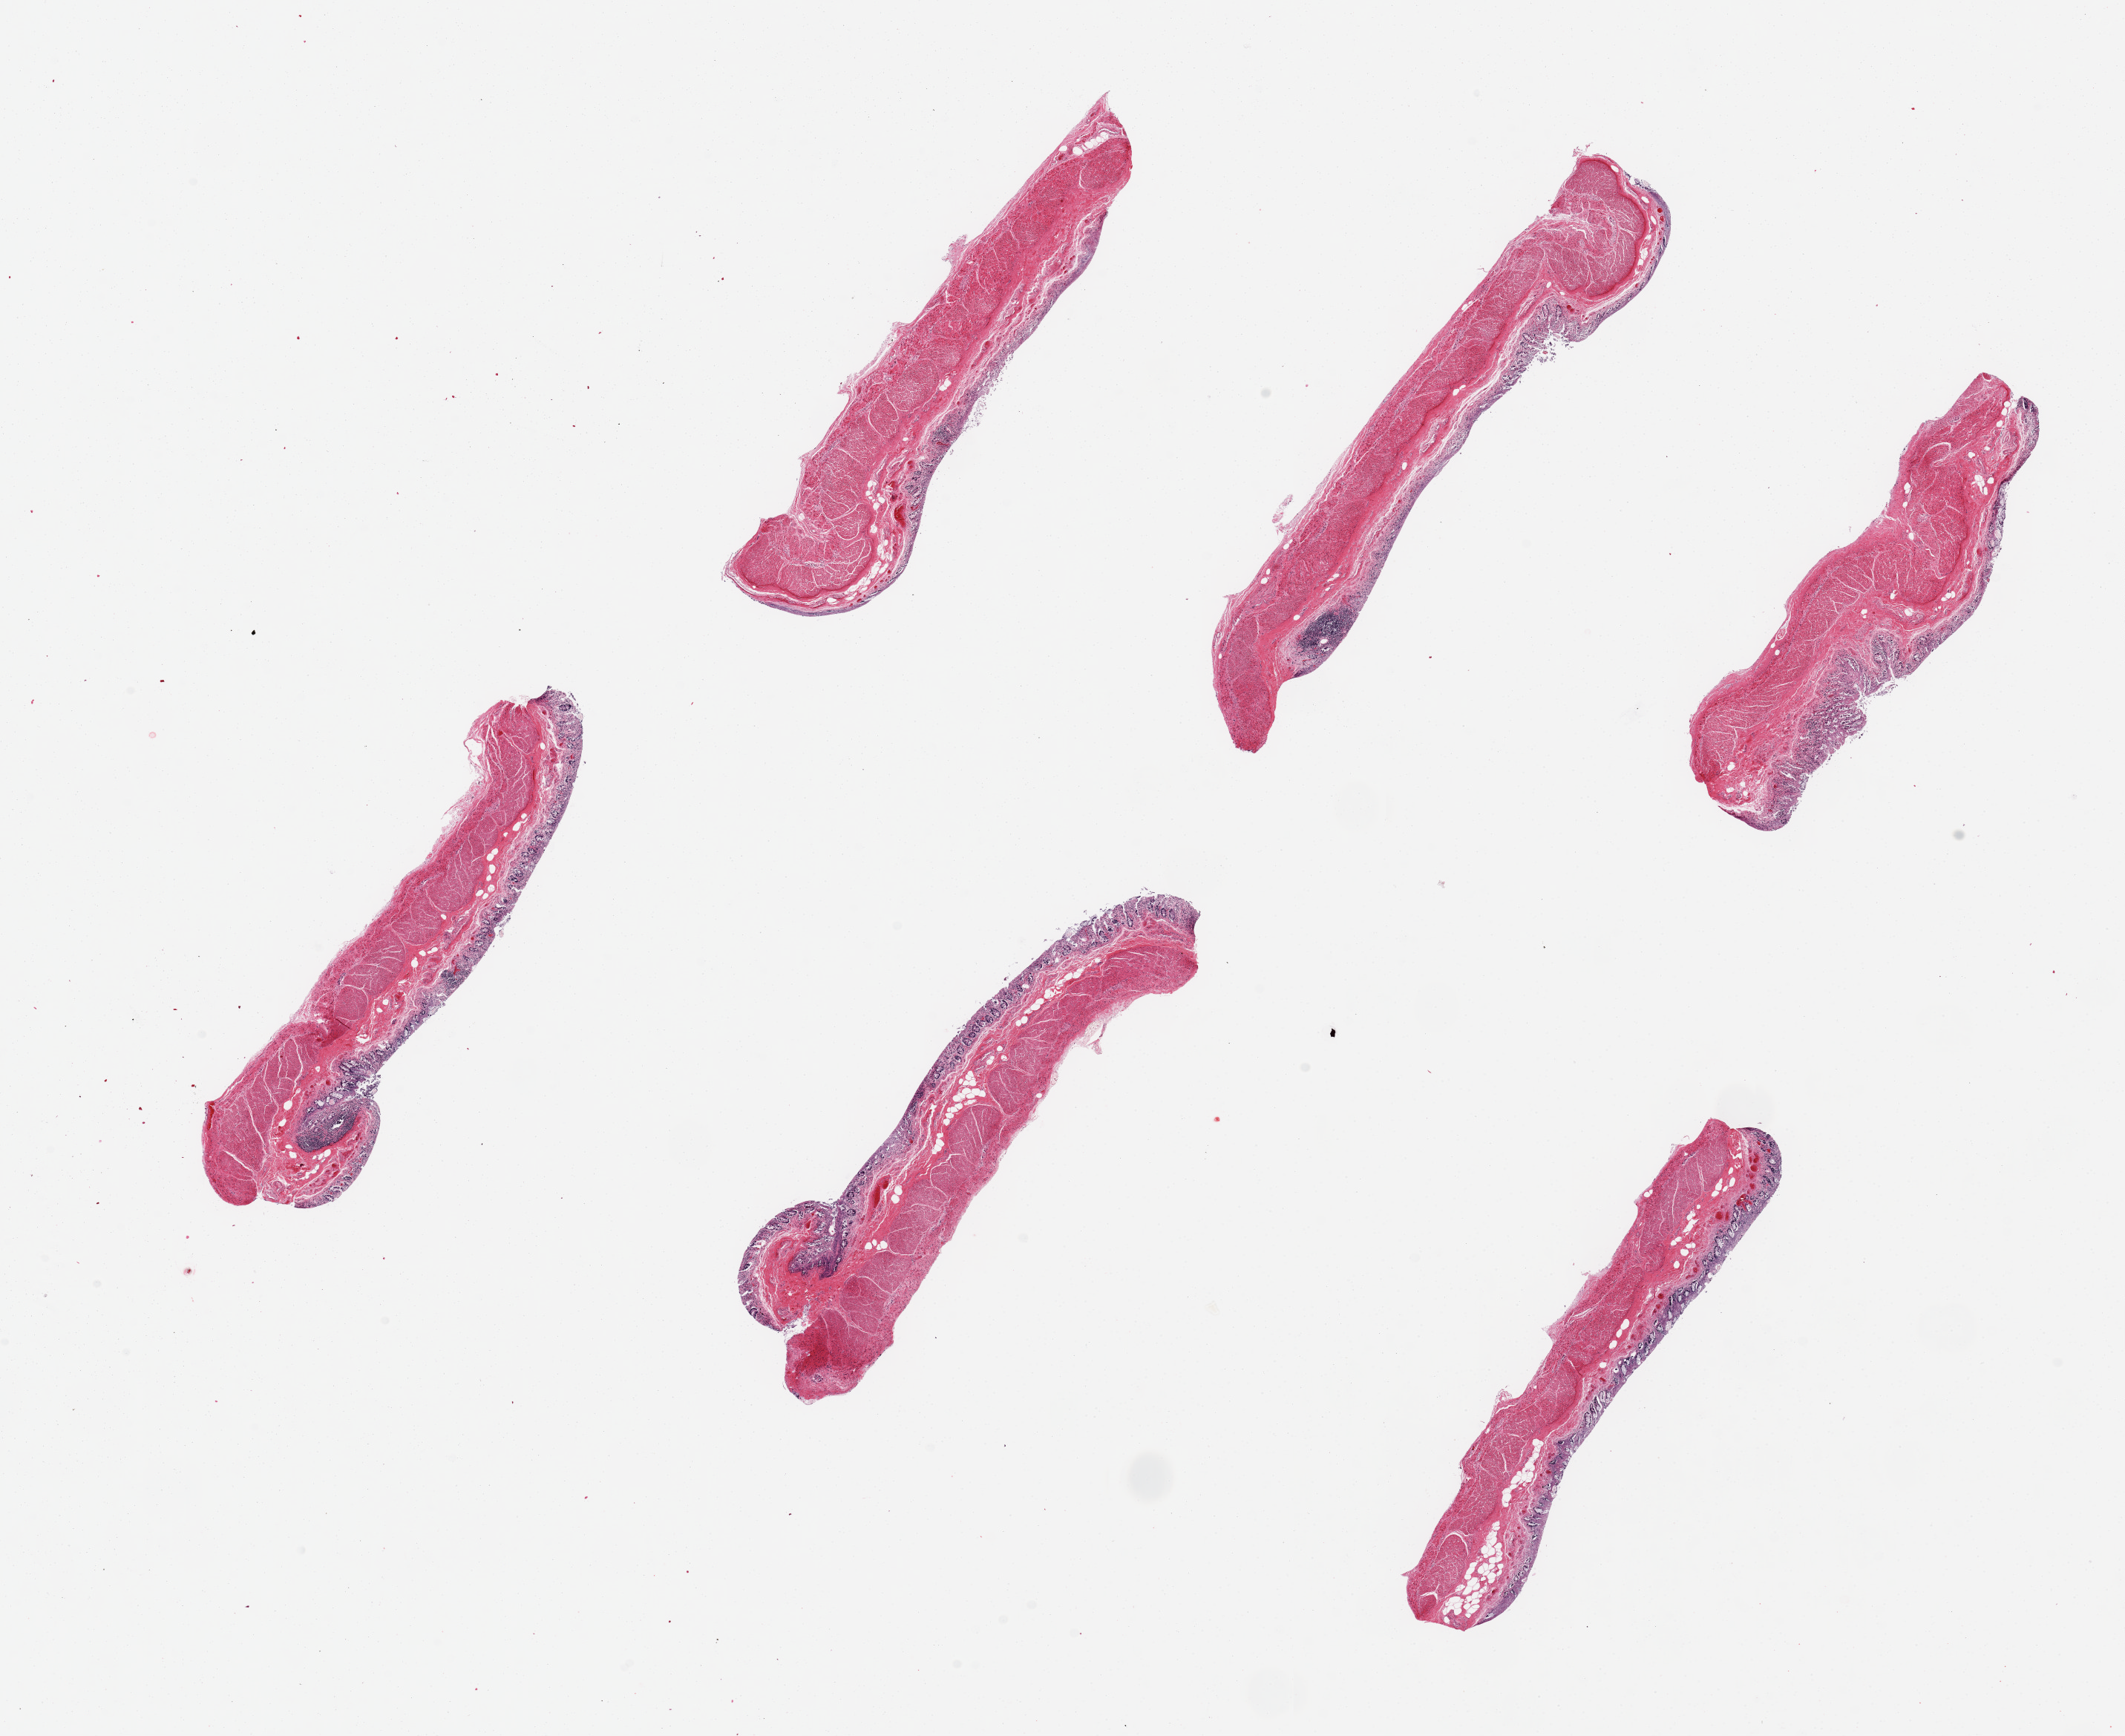
Digitized hematoxylin and eosin (H&E)-stained section, brightfield, a low-resolution overview of the entire scanned area, about 22.6 x 18.5 mm (acquisition: 20x scan), PAXgene-fixed paraffin-embedded (PFPE) section, section of transverse colon (target tissue), donor tissue sample.
- reviewer comment on this tissue sample: 6 pieces ~7x1.5mm, mucosa badly autolyzed &/or sloughing